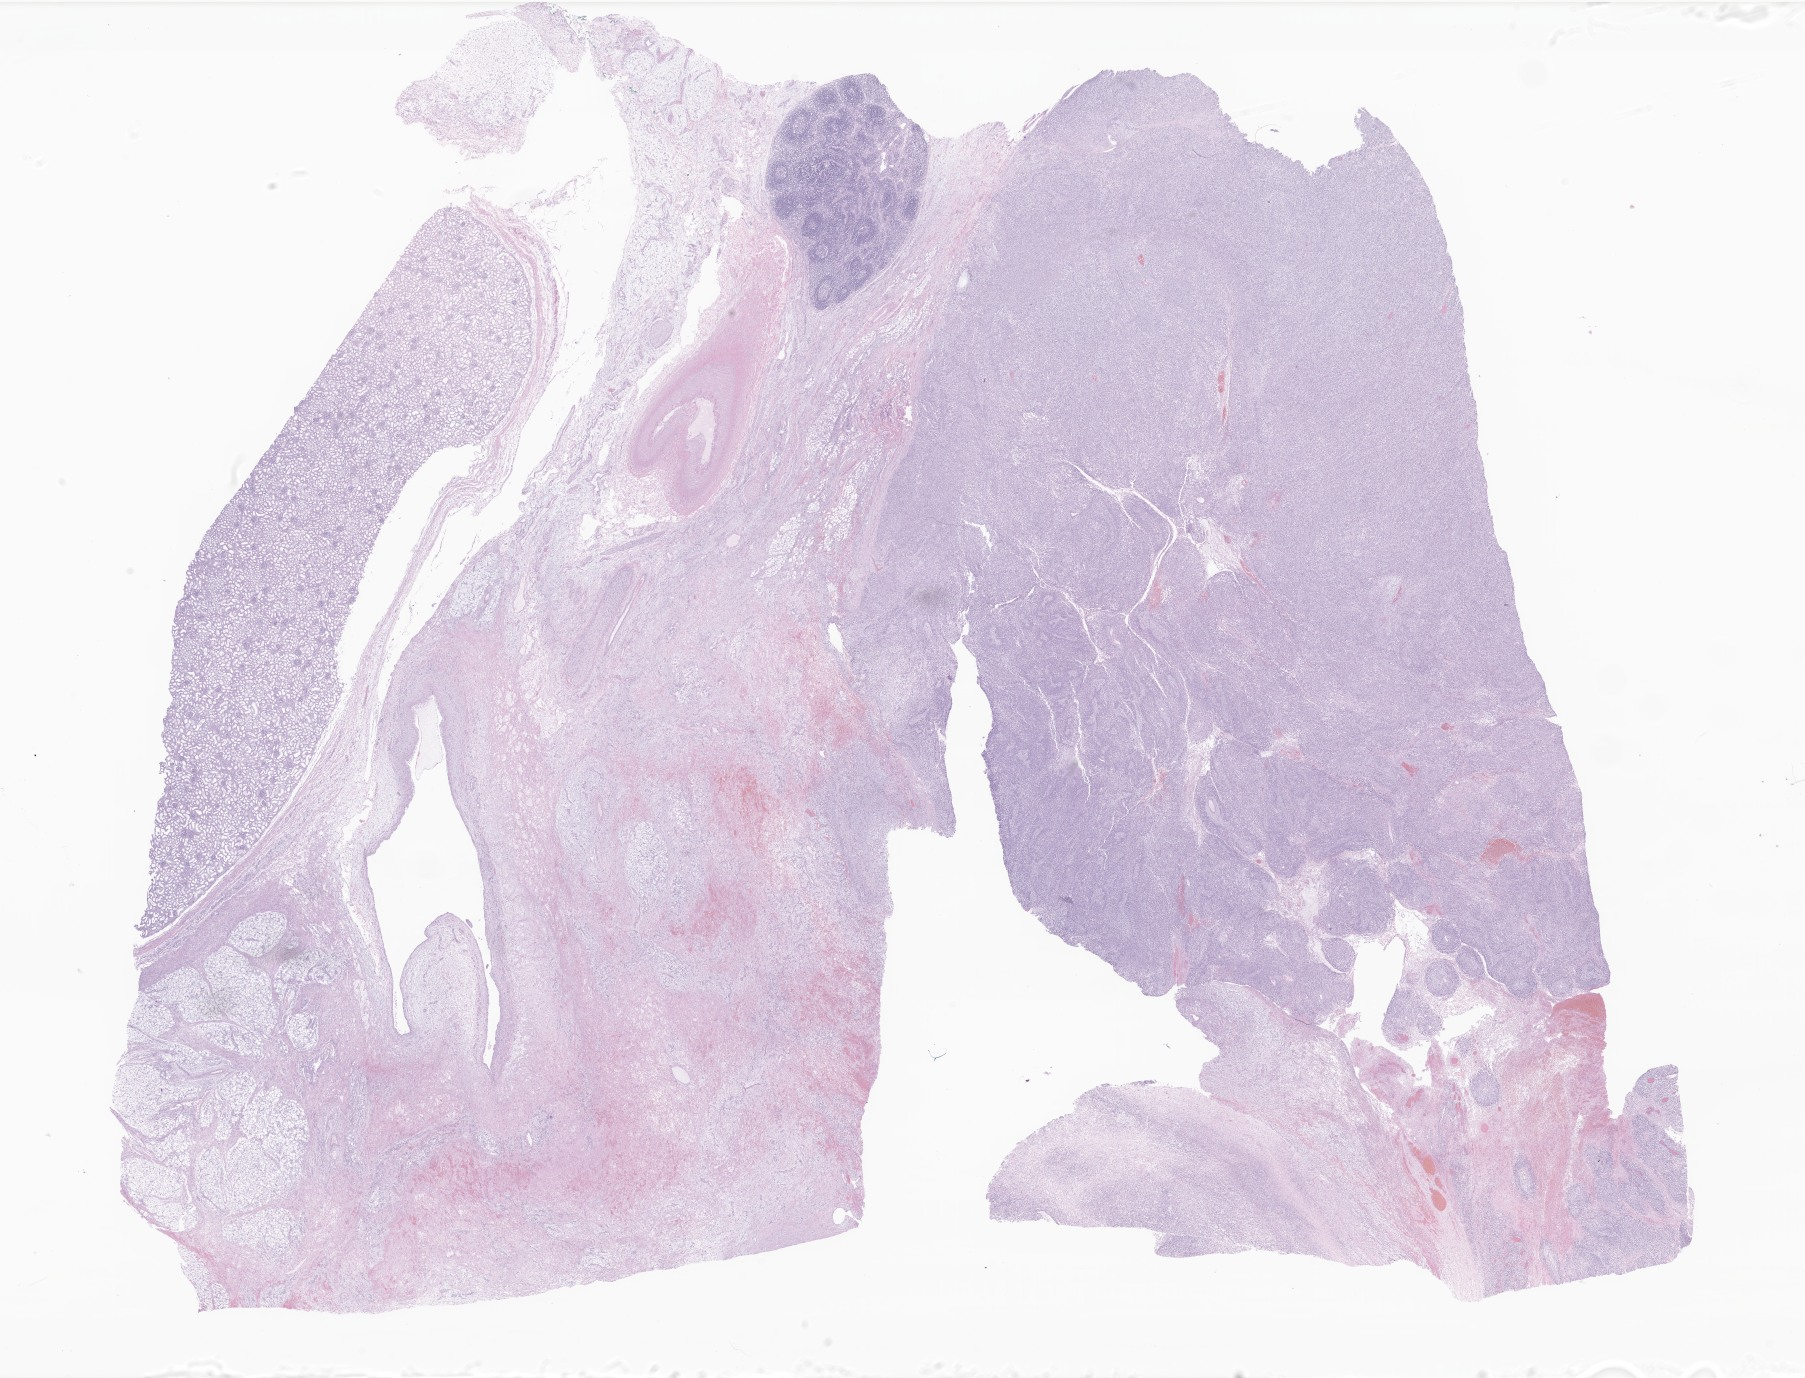
Whole-slide image, hematoxylin and eosin (H&E) stain of tumor tissue from the kidney, a low-resolution overview of the entire scanned area, about 30.4 x 23.2 mm. FFPE section. Patient male; age 763 days (about 2.1 years).
Recorded diagnosis: Rhabdomyosarcoma, NOS.